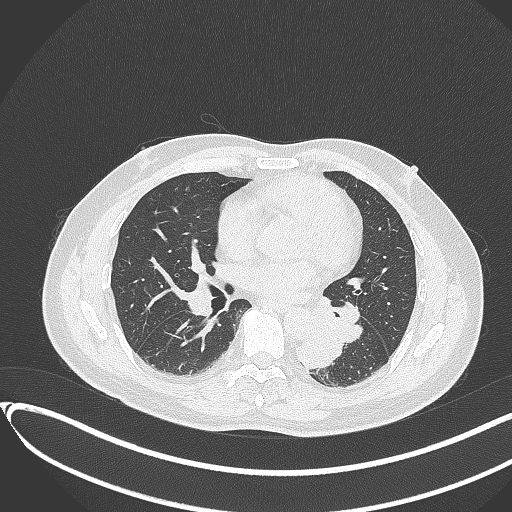
Chest CT, one axial slice. Slice 165 of 417 in the series (ordered by position). Reconstruction kernel B70f. Lung window (W 1500 / L -600 HU). 1 mm slice thickness. 512 × 512 image matrix. Male patient, age 54 years. Case-level facts recorded for this patient, not image findings: clinical TNM (as recorded): T3 N0 M0.
Annotated regions visible in this slice (rectangle marked by the reading radiologist):
- lung tumour (recorded histology: squamous cell carcinoma): bounding box [x1, y1, x2, y2] px = [299, 328, 348, 373]